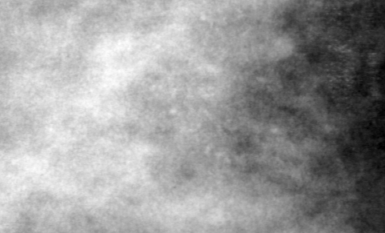
Cropped region of a digitized screen-film mammogram centred on a radiologist-marked abnormality; left breast; CC view; BI-RADS breast density category 3 (scale 1–4).
Marked abnormality: calcifications, morphology pleomorphic, distribution clustered; BI-RADS assessment category 4; pathology (as recorded): benign.